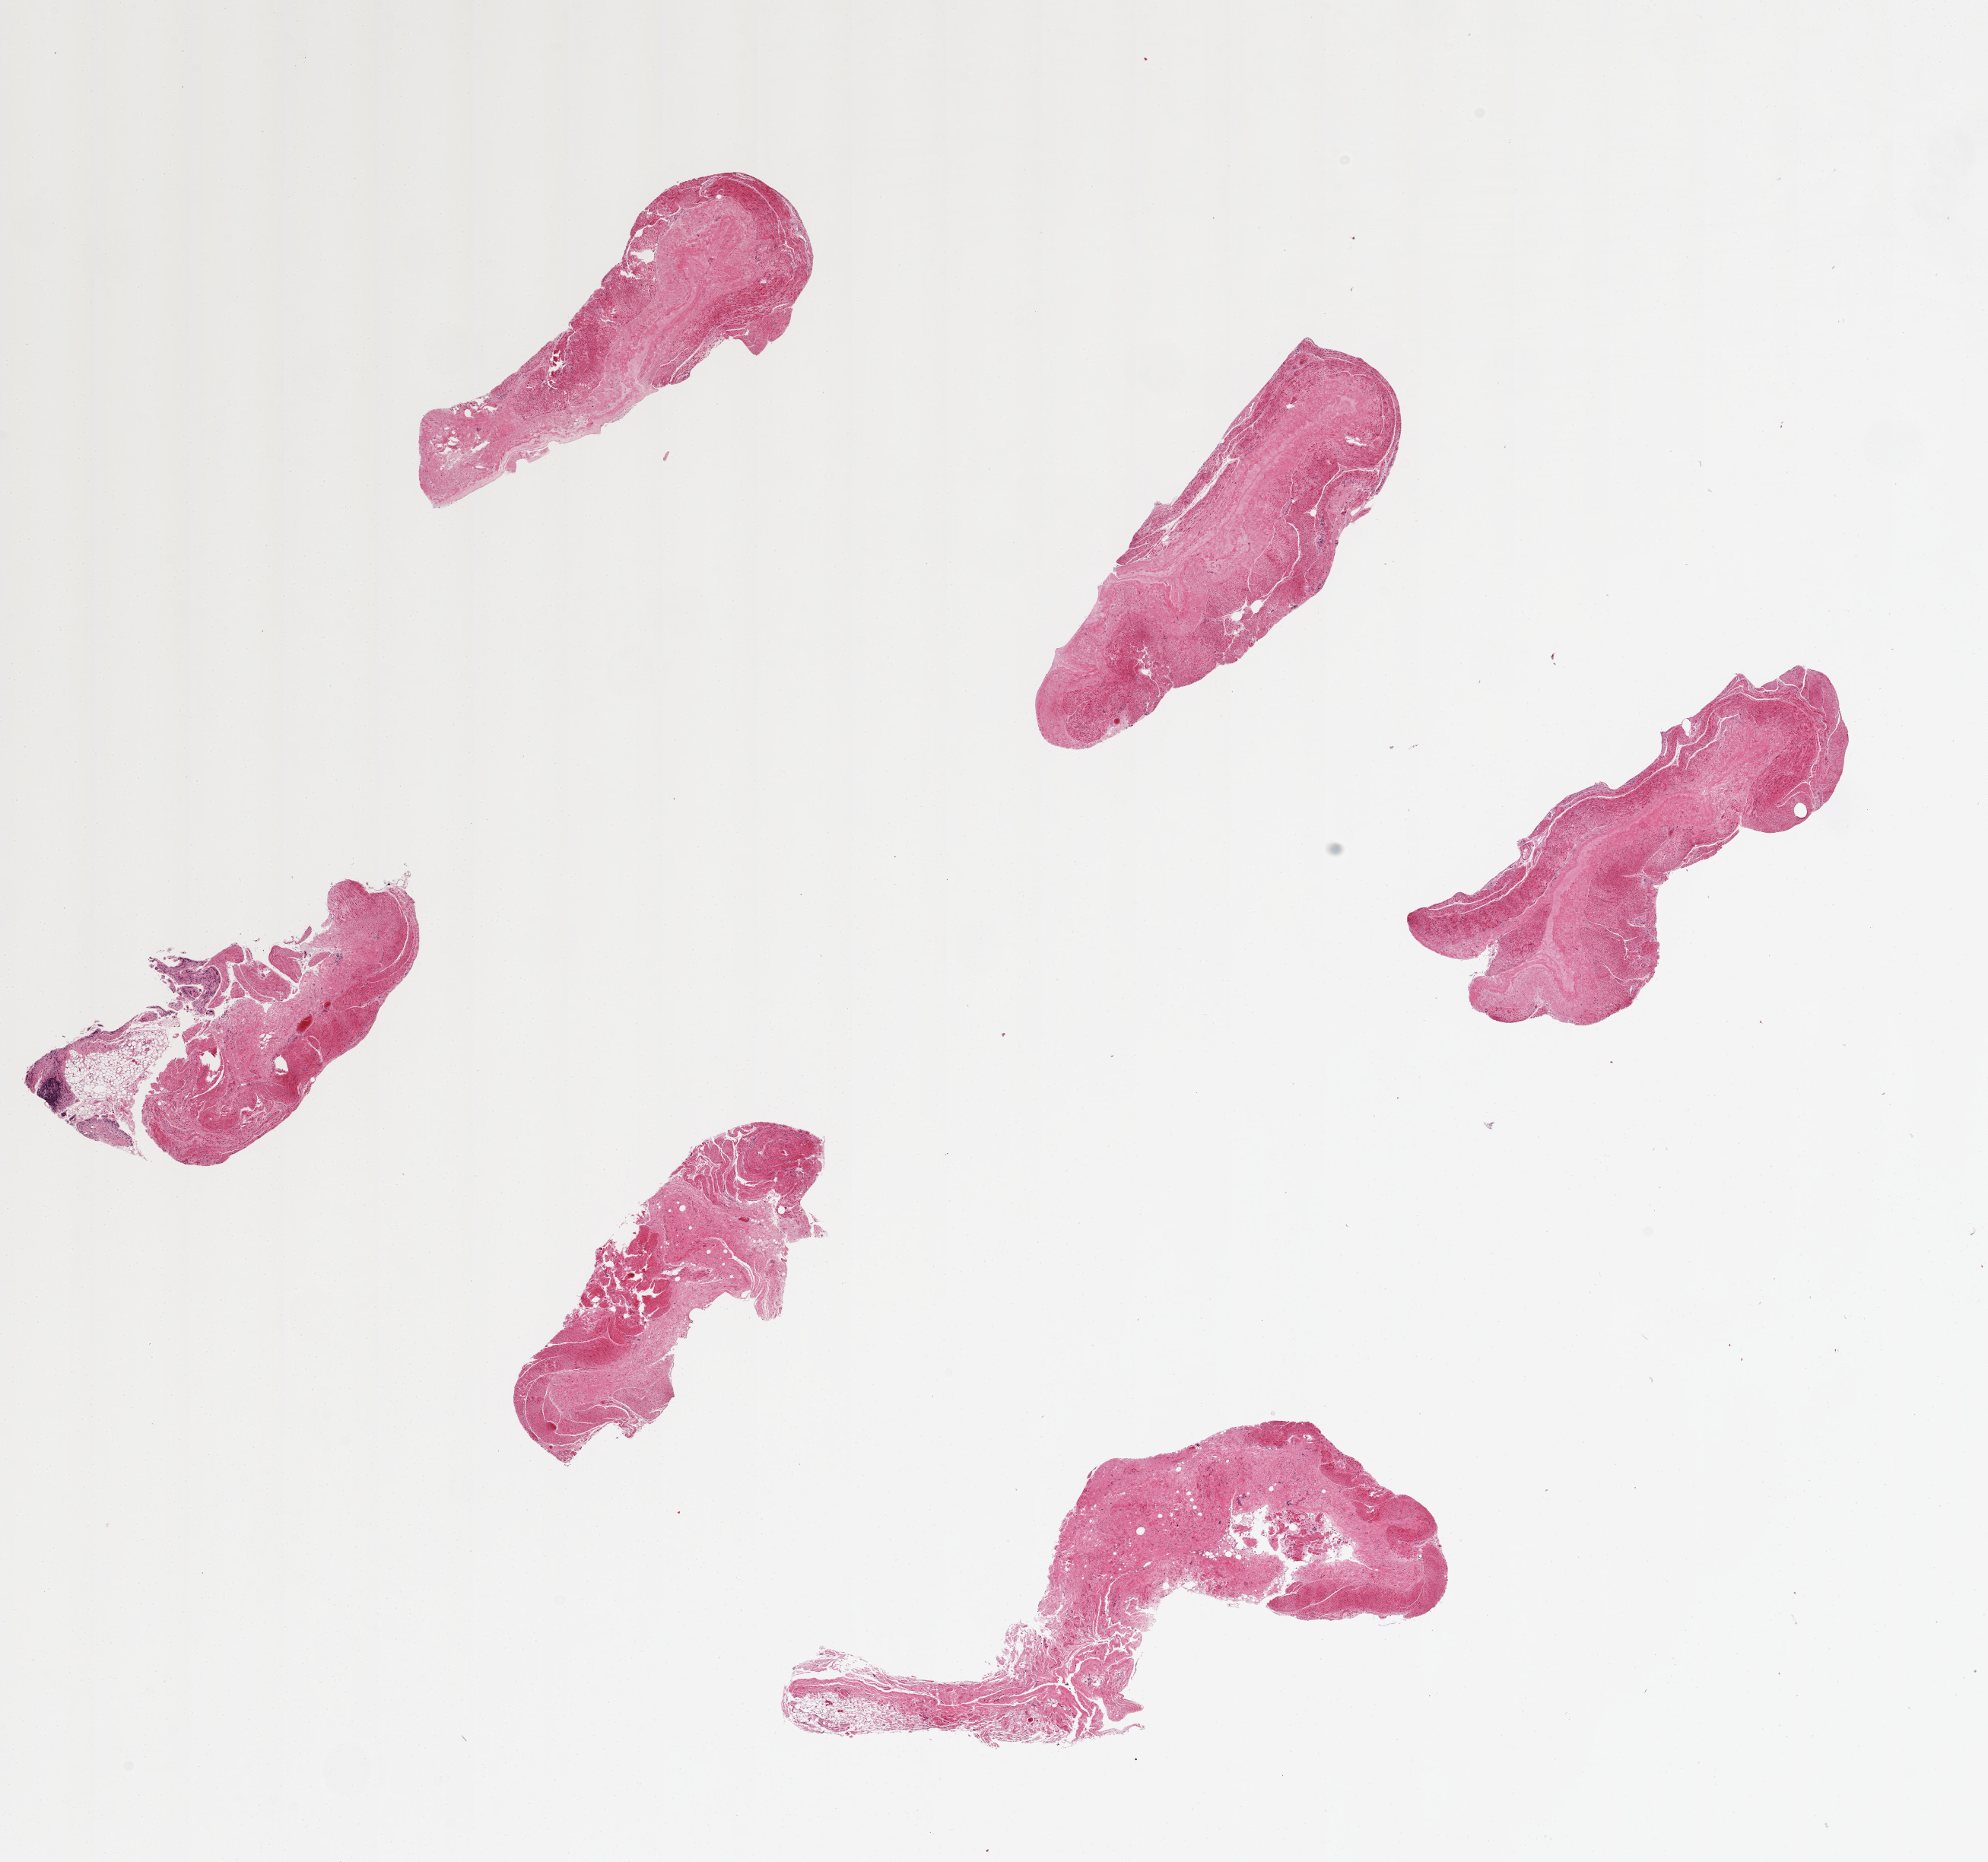
Whole-slide image, hematoxylin and eosin (H&E) stain, shown as a low-resolution overview of the whole scanned area (about 20.7 x 19.4 mm, acquisition: 20x scan), PAXgene-fixed paraffin-embedded (PFPE) section, section of ileum (target tissue), donor tissue sample. Donor: male.
Pathologist's review note for this sample: 6 pieces; essentially no intact mucosa, muscularis present.